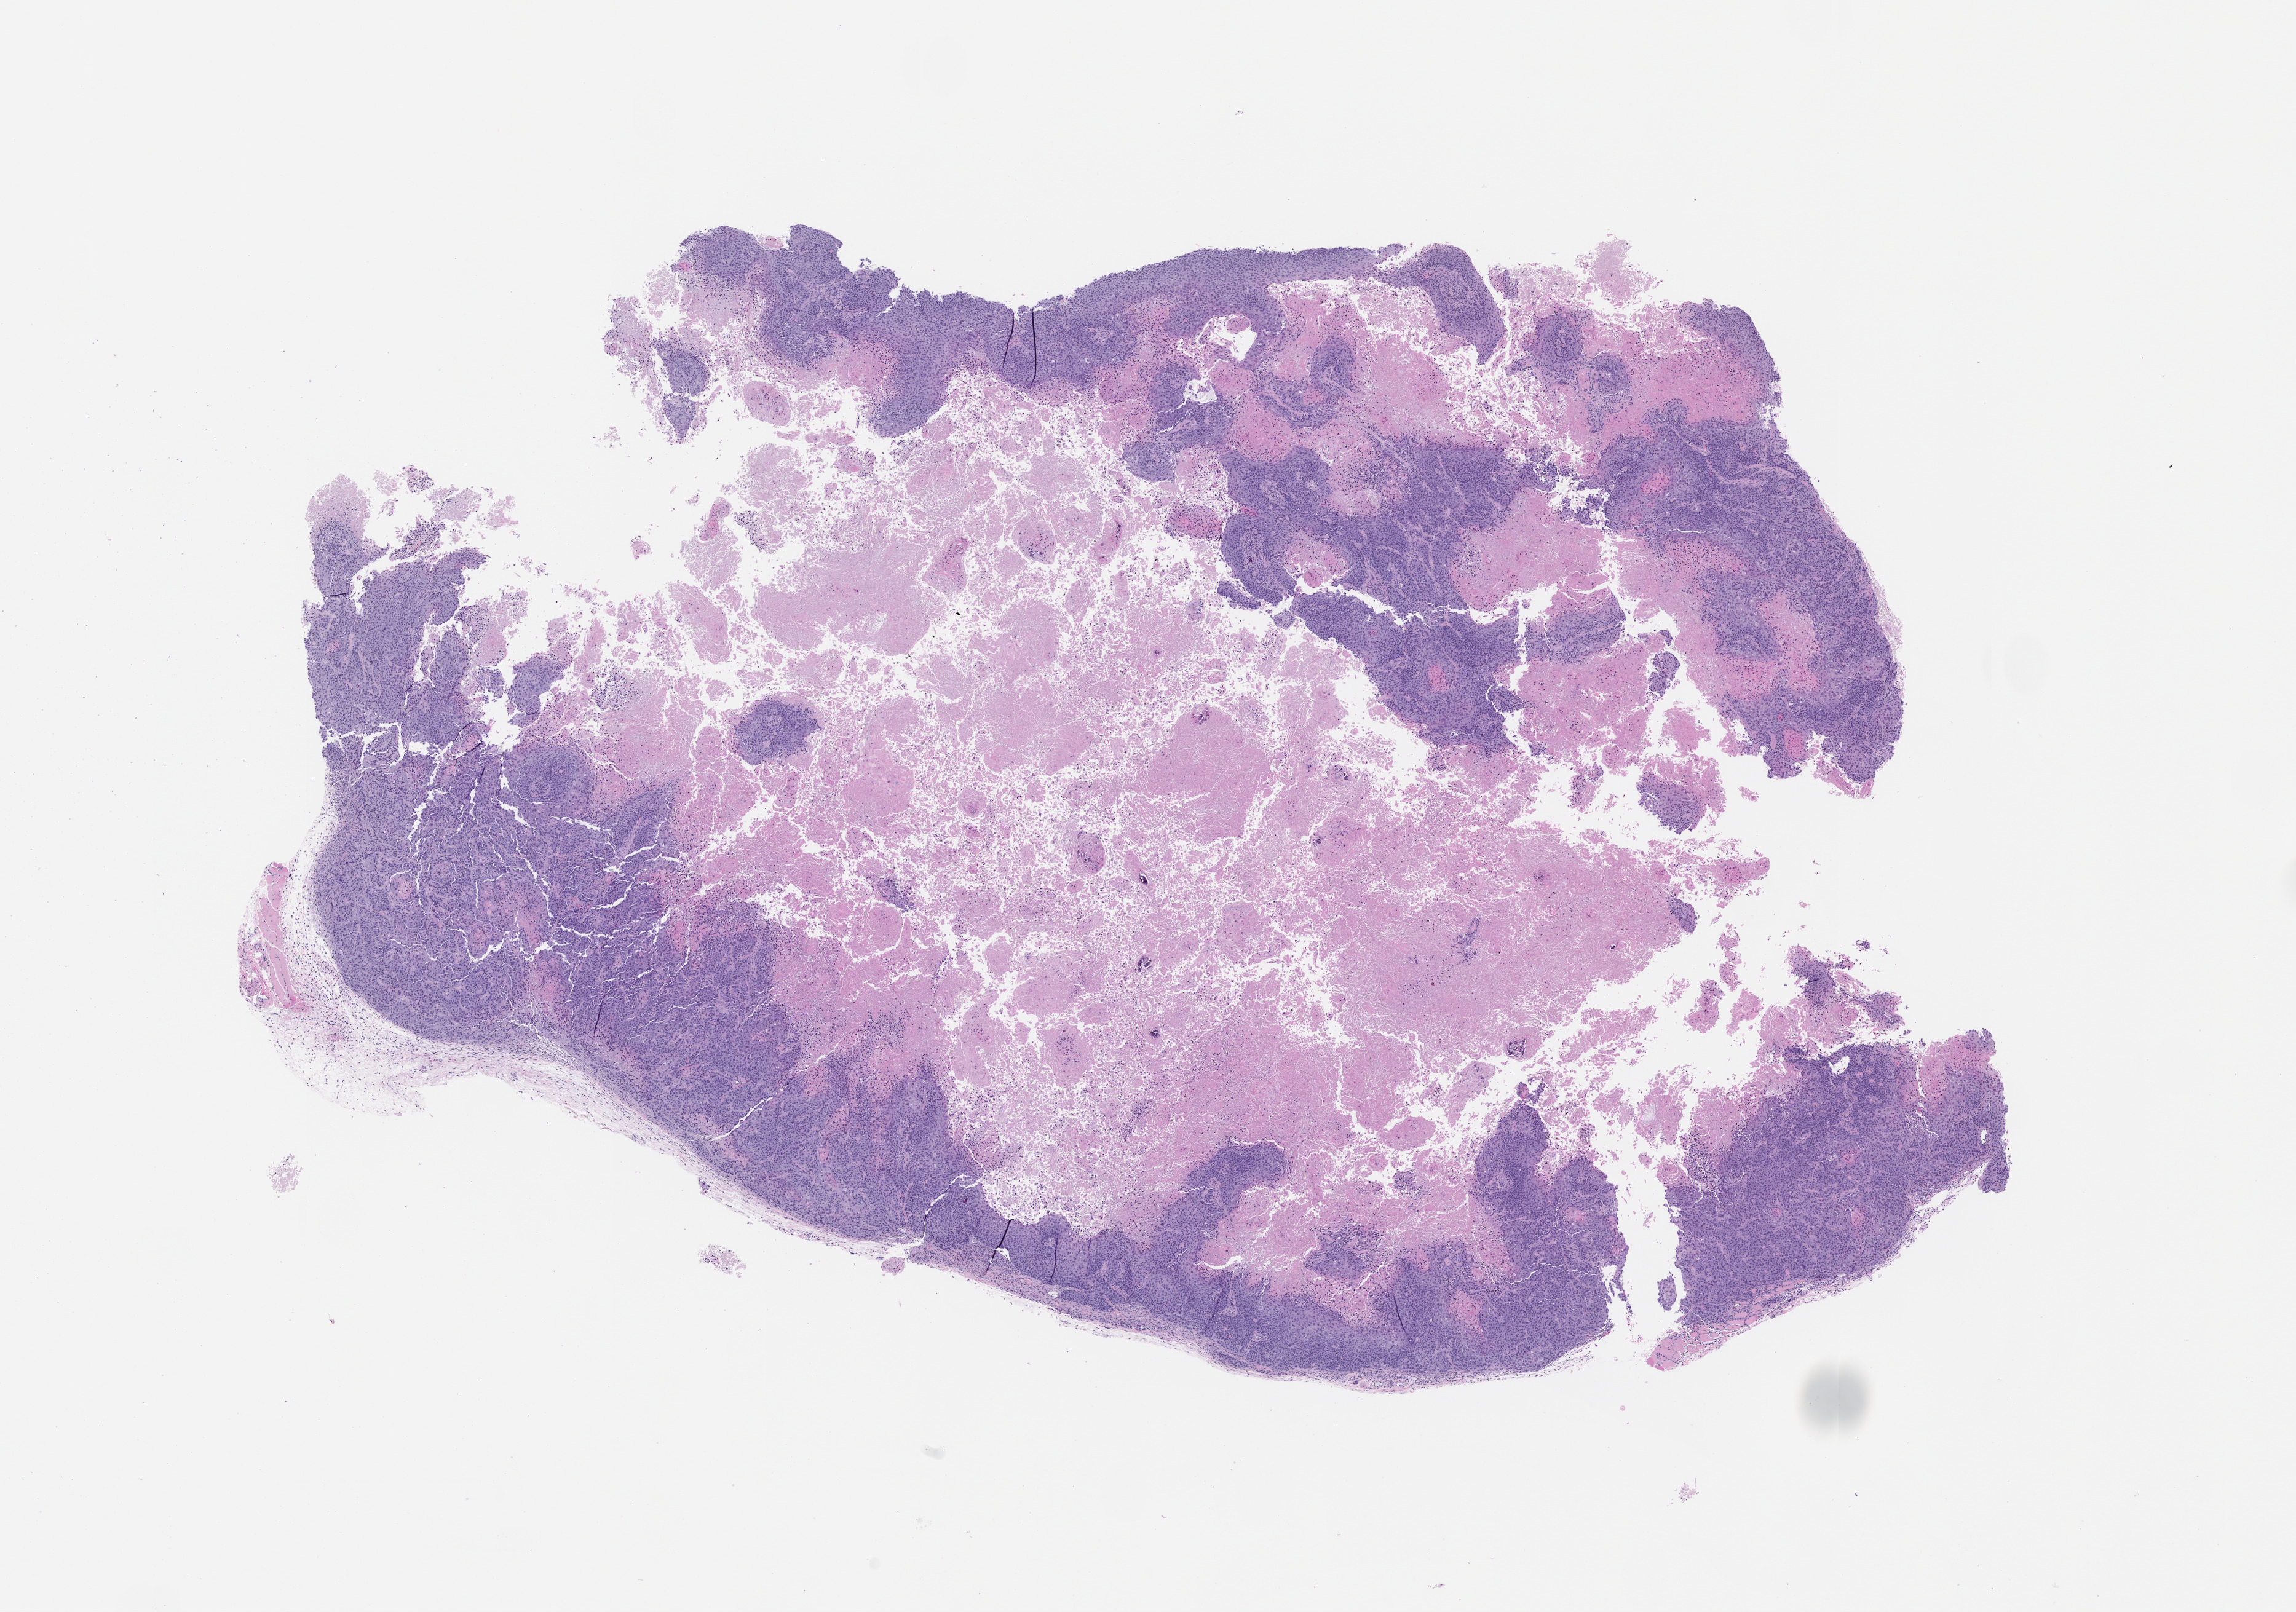
Hematoxylin and eosin (H&E) whole-slide image of a patient-derived xenograft (PDX) tumor grown in a mouse, passage 1, a low-resolution overview of the entire scanned area, about 15.0 x 10.5 mm, FFPE section, originating tumor site category: bladder.
Originating patient diagnosis: Urothelial Carcinoma.